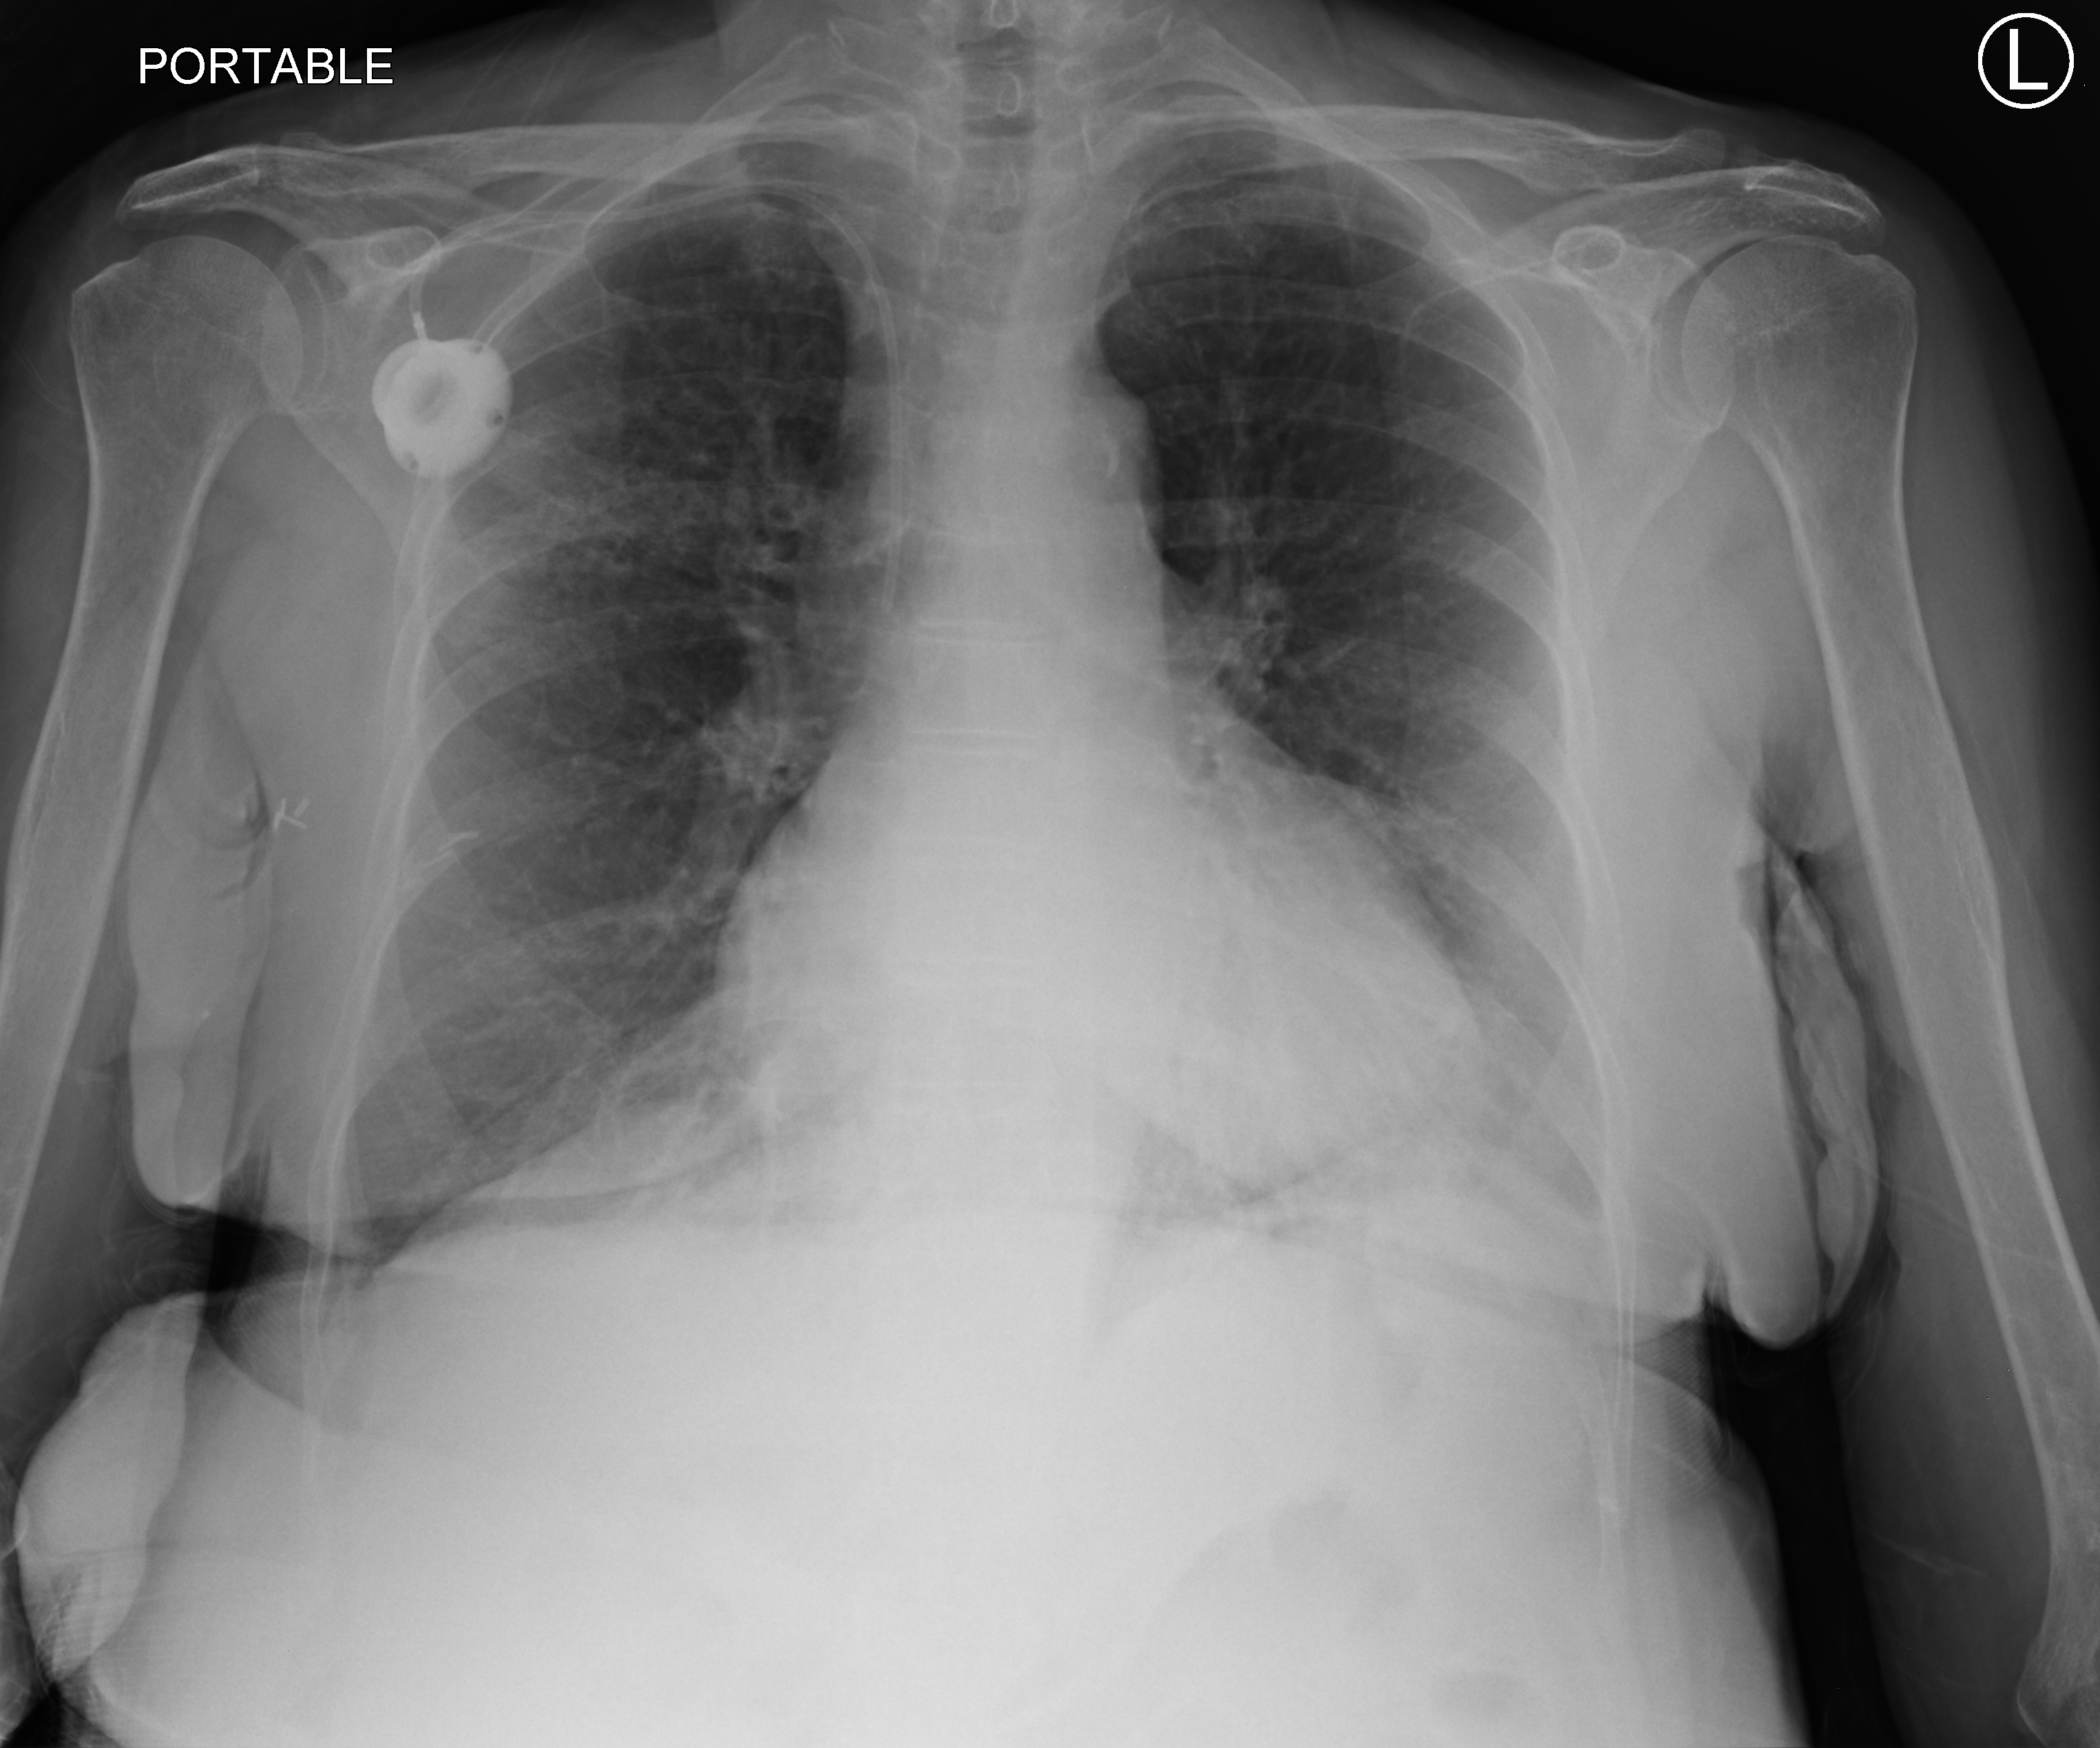
Bedside chest radiograph (computed radiography), anteroposterior (AP) projection. Patient hospitalised with COVID-19; female, aged 60–74 years.
Admission-level facts for this patient (not findings on this image; timing relative to this image not recorded):
- length of hospital stay: 43 days
- smoking status (admission record): former
- admitted to intensive care during this hospital stay: yes